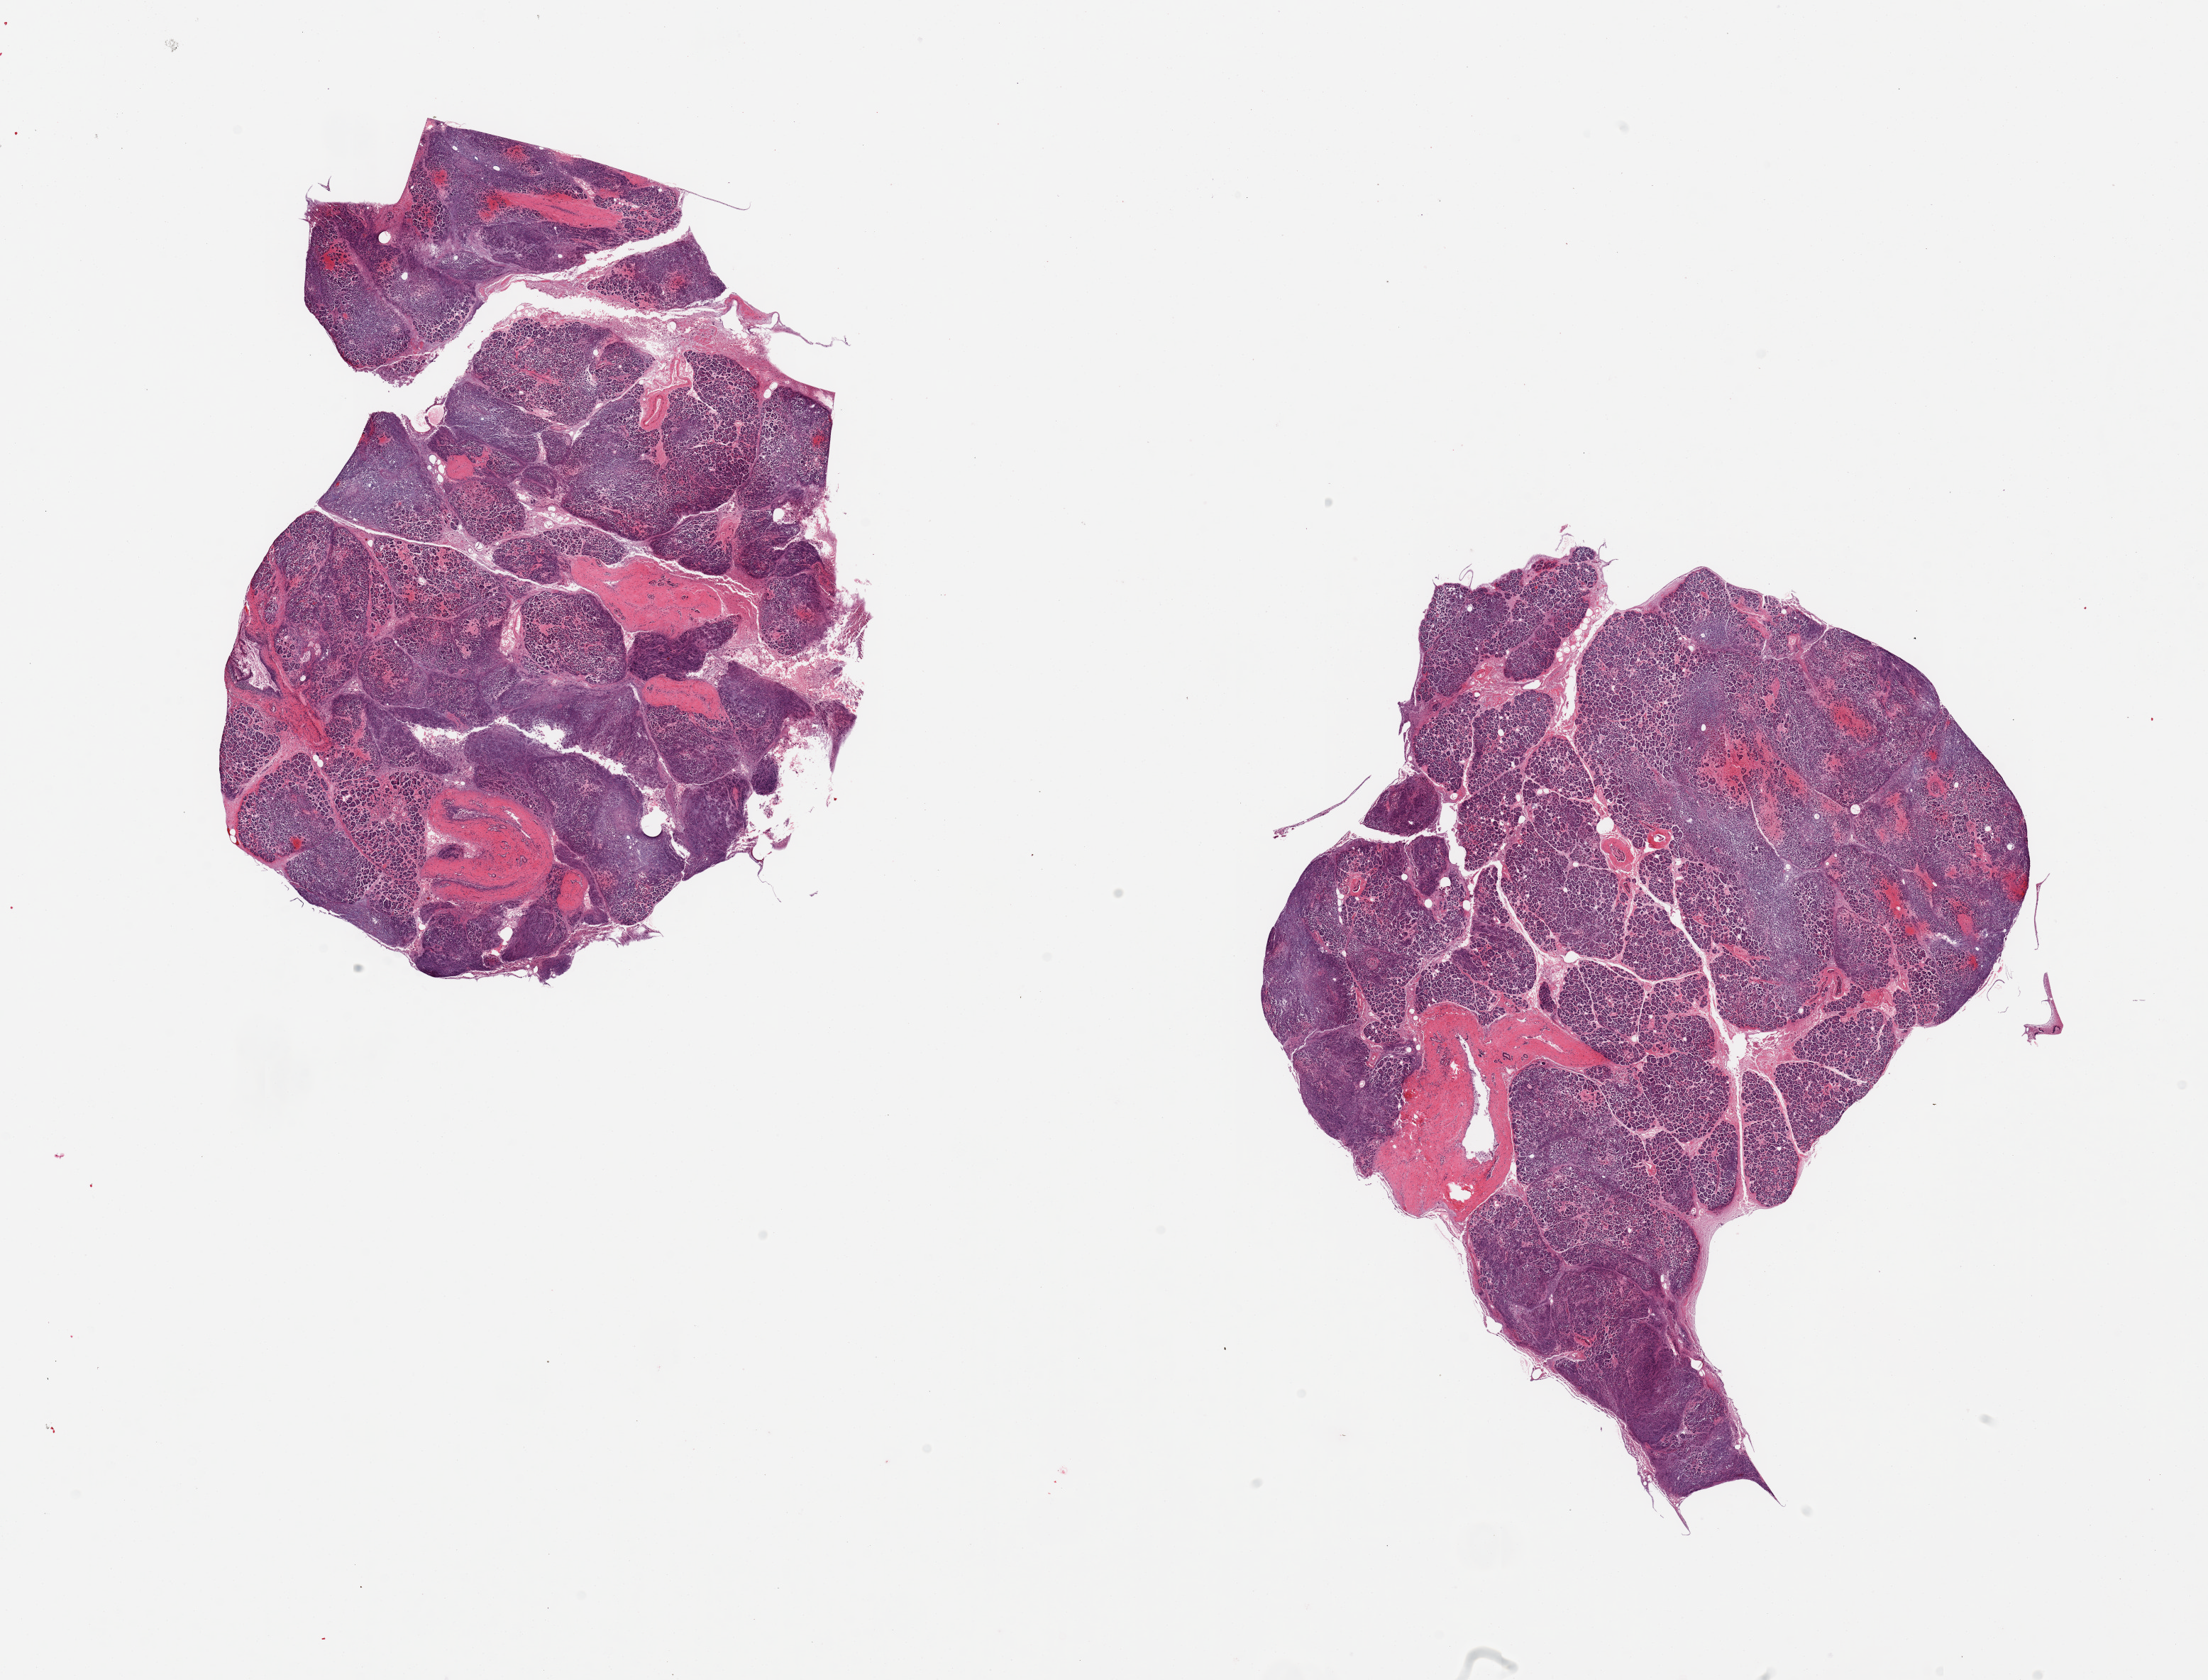
Whole-slide image, hematoxylin and eosin (H&E) stain — low-resolution overview of the scanned area, about 24.6 x 18.7 mm; PAXgene-fixed paraffin-embedded (PFPE) section; sampled site (target tissue): pancreas; tissue donor sample. Female donor.
Pathologist's review note for this sample: 2 pieces, moderately advanced saponification/autolysis.